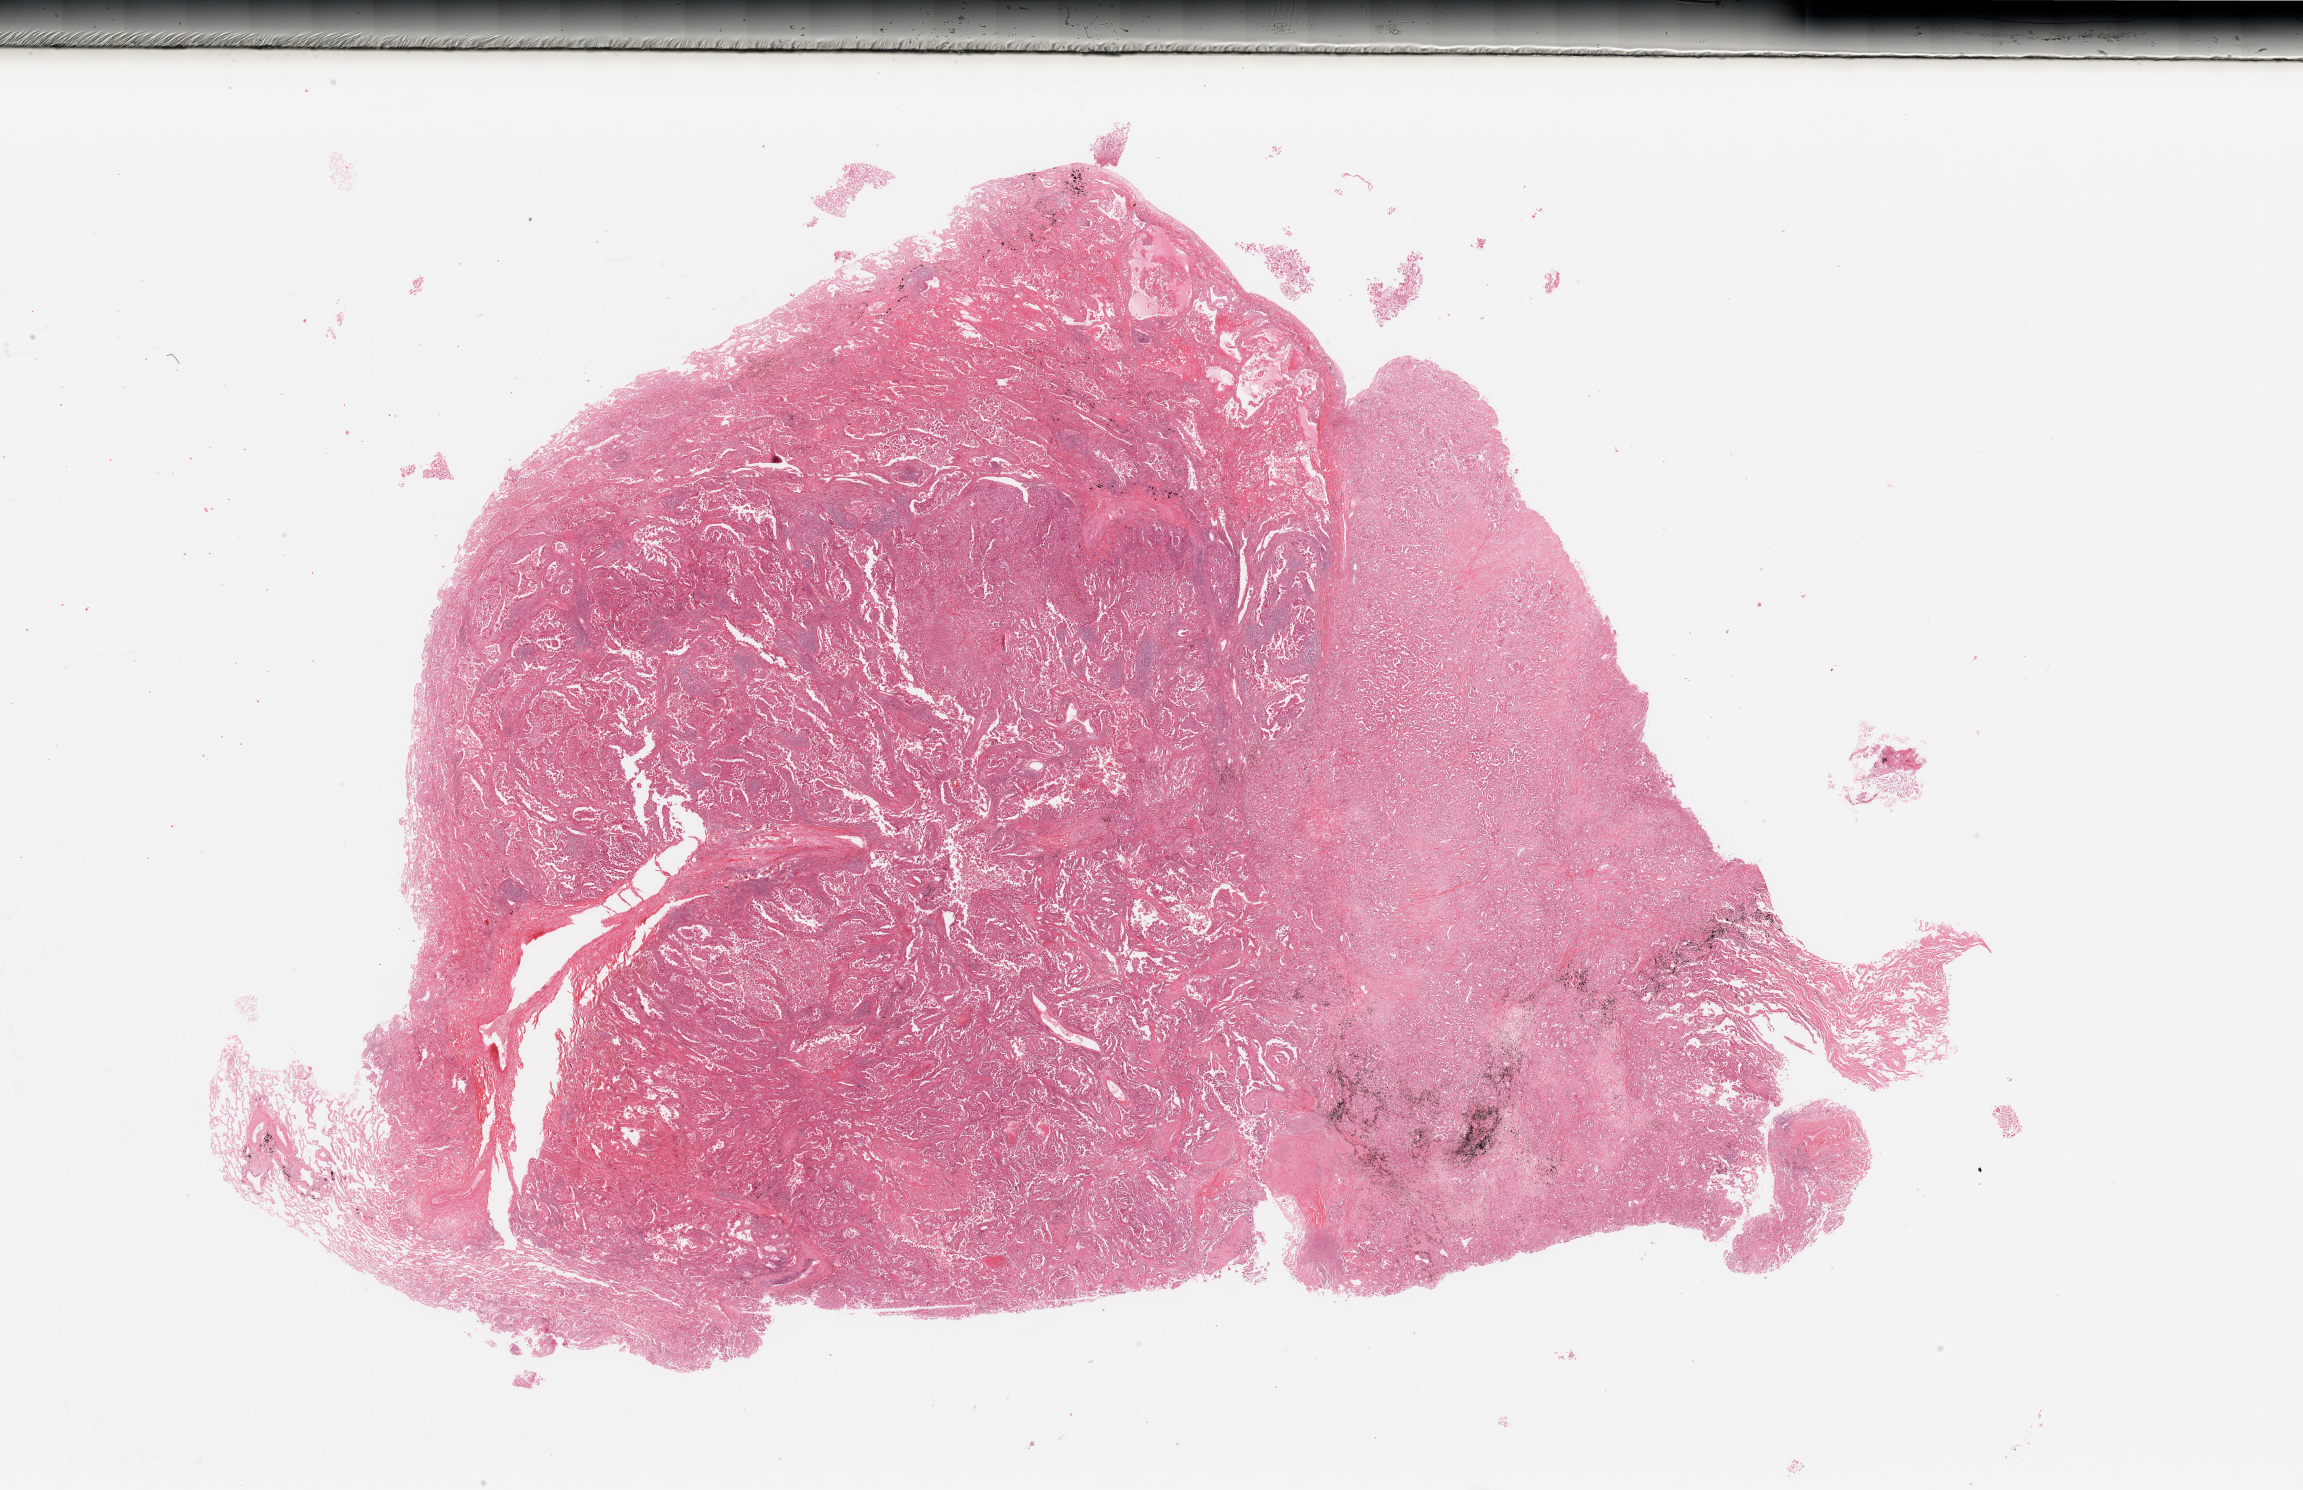
Whole-slide histology image, H&E, low-resolution overview of the scanned area, about 36.4 x 23.6 mm, lung, tumour tissue. Patient: male, age 59 years. Histologic grade: G2 (moderately differentiated).
Diagnosis: Adenocarcinoma, NOS. AJCC pathologic stage: IIIA.